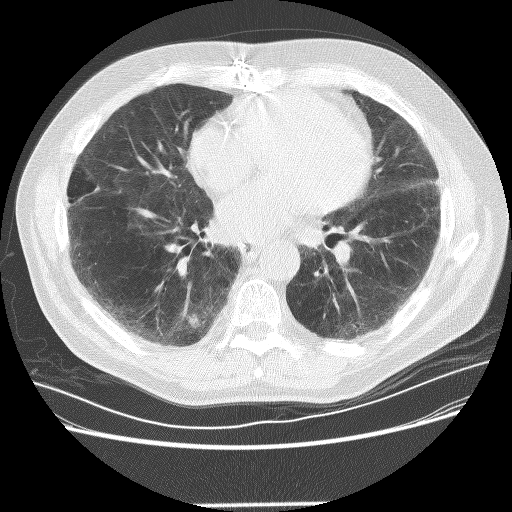
Chest CT (low-dose screening protocol), one axial image, baseline screening round, lung window (W 1500 / L -600 HU), lung (sharp) reconstruction kernel (BONE), slice 146 of 281 in the series, 512 × 512 image matrix. Male, age 72 years at enrolment.
• Expert-annotated lung lesion, bounding box [x1, y1, x2, y2] px = [171, 307, 210, 343].
• The screening reader recorded 2 non-calcified nodules or masses ≥4 mm on this exam (right lower lobe, left lower lobe); which of them this box marks is not recorded.
• Official screen result: positive, change unspecified: nodule(s) >= 4 mm or enlarging nodule(s), mass(es), or other non-specific abnormalities suspicious for lung cancer.
• Later outcome: lung cancer diagnosed 436 days after this screen — squamous cell carcinoma, NOS, right lower lobe, poorly differentiated (G3), stage IB (AJCC 6th edition), 42 mm at pathology.